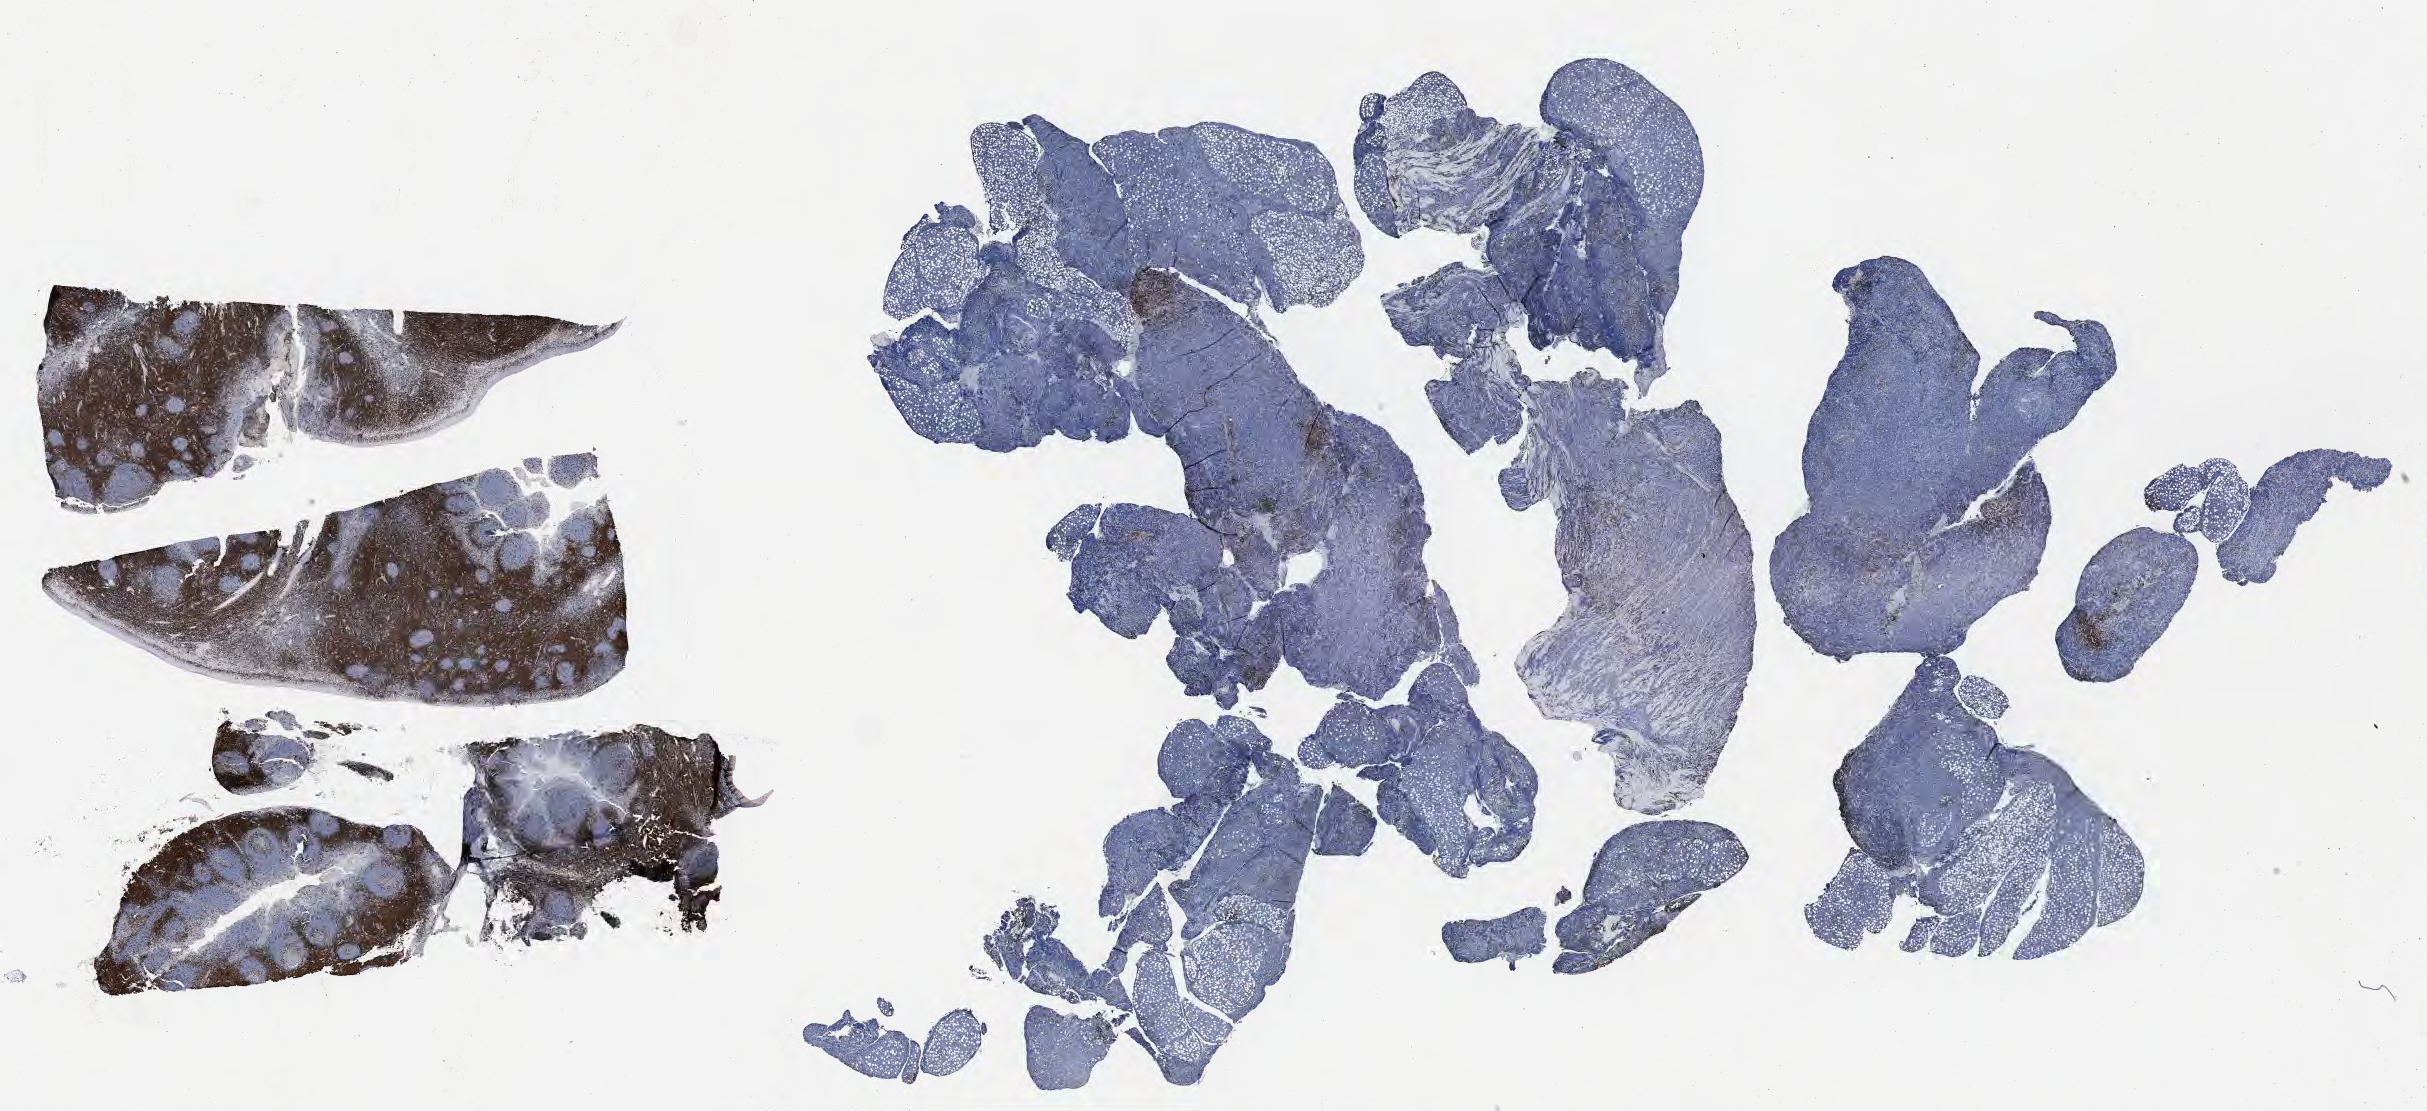
Immunohistochemistry (IHC) whole-slide image stained for CD3, shown as a low-resolution overview of the whole scanned area (about 39.2 x 18.0 mm). Tumor tissue. Anatomic site: abdomen proper. Male patient; age at initial diagnosis 4 years.
* histologic diagnosis: Burkitt lymphoma, NOS